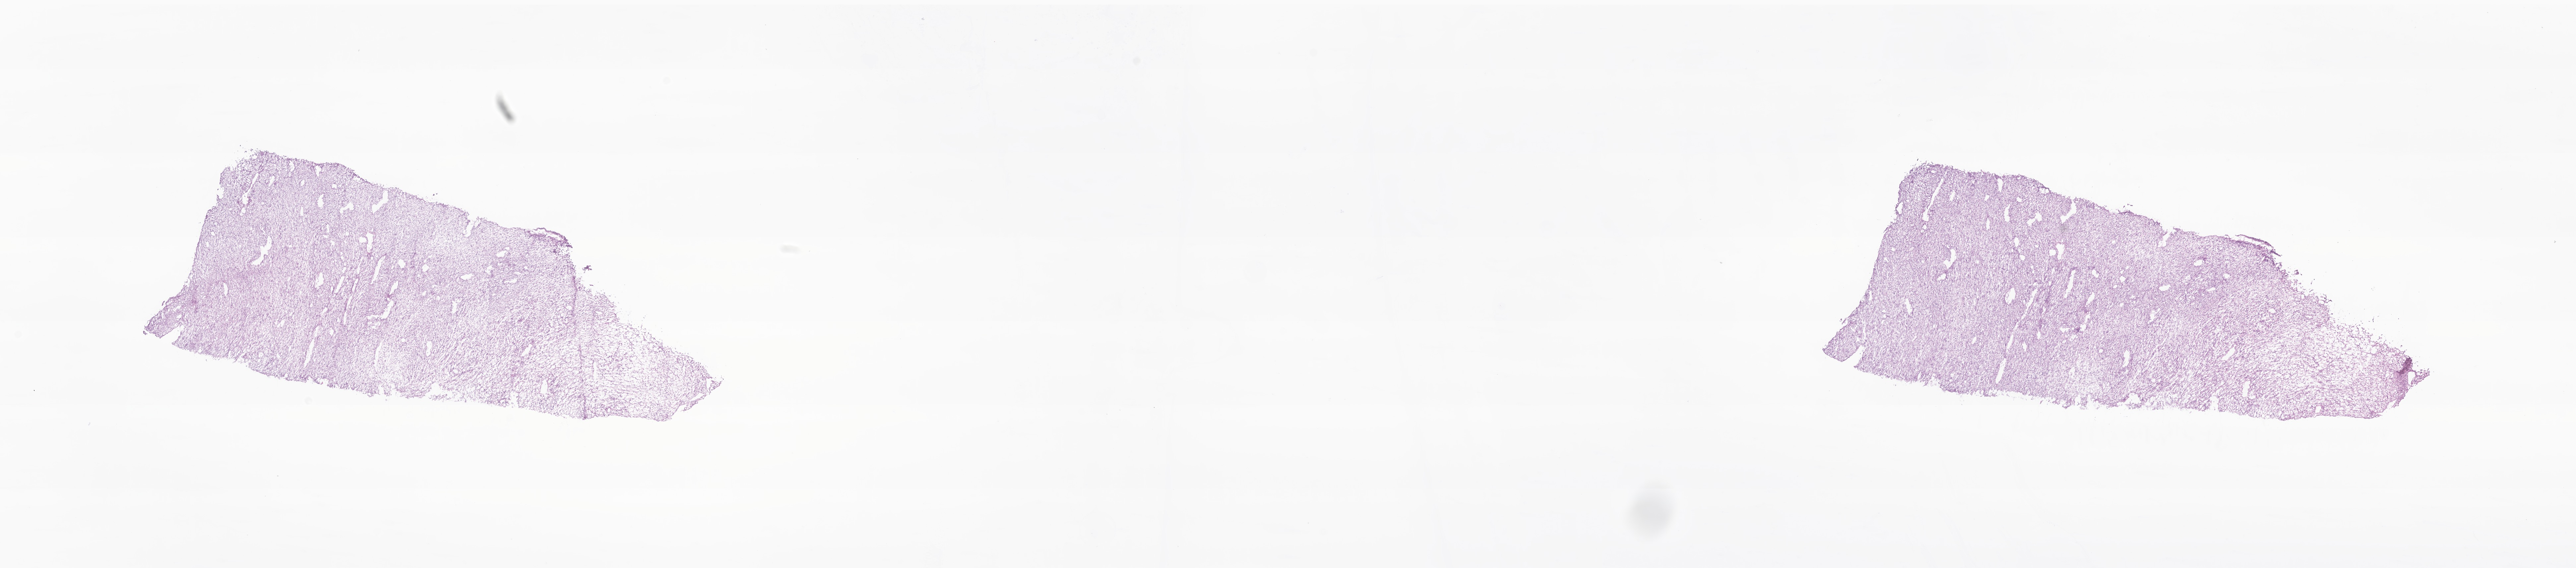
H&E whole-slide image of tumor tissue from the nerve of thorax, a low-resolution overview of the entire scanned area, about 32.7 x 7.2 mm. Cryosection (OCT / tissue freezing medium). Female patient, age 185 months (15 years 5 months).
- diagnosis (ICD-O-3 morphology term): Sarcoma, NOS